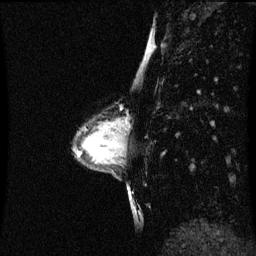
Breast MRI (dynamic contrast-enhanced), one sagittal slice; position 26 of 60 along the scan axis; dynamic contrast-enhanced series, image 2 of 3 at this slice position (ordered by acquisition); 1.5 T; TE 4.2 ms, TR 8.9 ms; 256 × 256 image matrix. Patient: female, 33 years. From the clinical record (not read from this slice): setting: breast cancer imaged before/during neoadjuvant chemotherapy; receptor status: HER2-positive.
Outlined on this slice (semi-automatically segmented with operator editing):
- analysis volume of interest (the breast-tissue region the enhancement analysis was run in; not a lesion): box from (x=107, y=116) to (x=125, y=147) px
- tumour enhancement mask (voxels above the 70 % enhancement threshold inside the analysis volume of interest): (x=110, y=122)–(x=122, y=127)